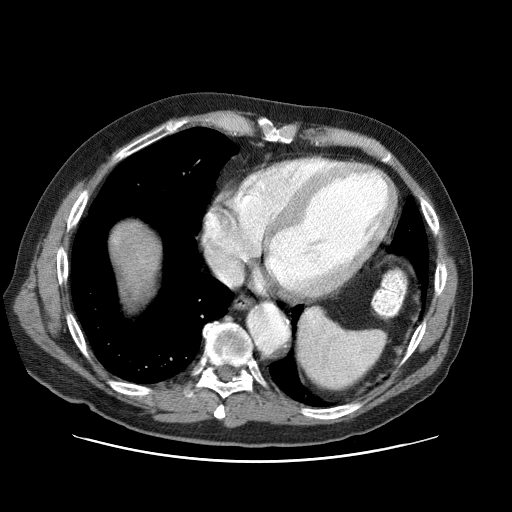
Contrast-enhanced abdominal CT (liver protocol), one axial slice; reconstruction kernel STANDARD; 120 kVp; one of 3 acquisitions stored at this slice position; soft-tissue window (W 400 / L 40 HU); 512 × 512 image matrix, field of view 400 × 400 mm. Case-level facts recorded for this patient, not image findings: diagnosis: hepatocellular carcinoma (patient treated with transarterial chemoembolisation; whether this scan precedes or follows treatment is not stated here); TNM stage (as recorded): Stage-IIIA.
Outlined on this slice (semi-automatically segmented with operator editing):
- liver parenchyma outside the tumour (the mass and vessels are separate outlines, so this box may not span the whole liver): bounding box <110,220,161,301> (left, top, right, bottom; pixels)